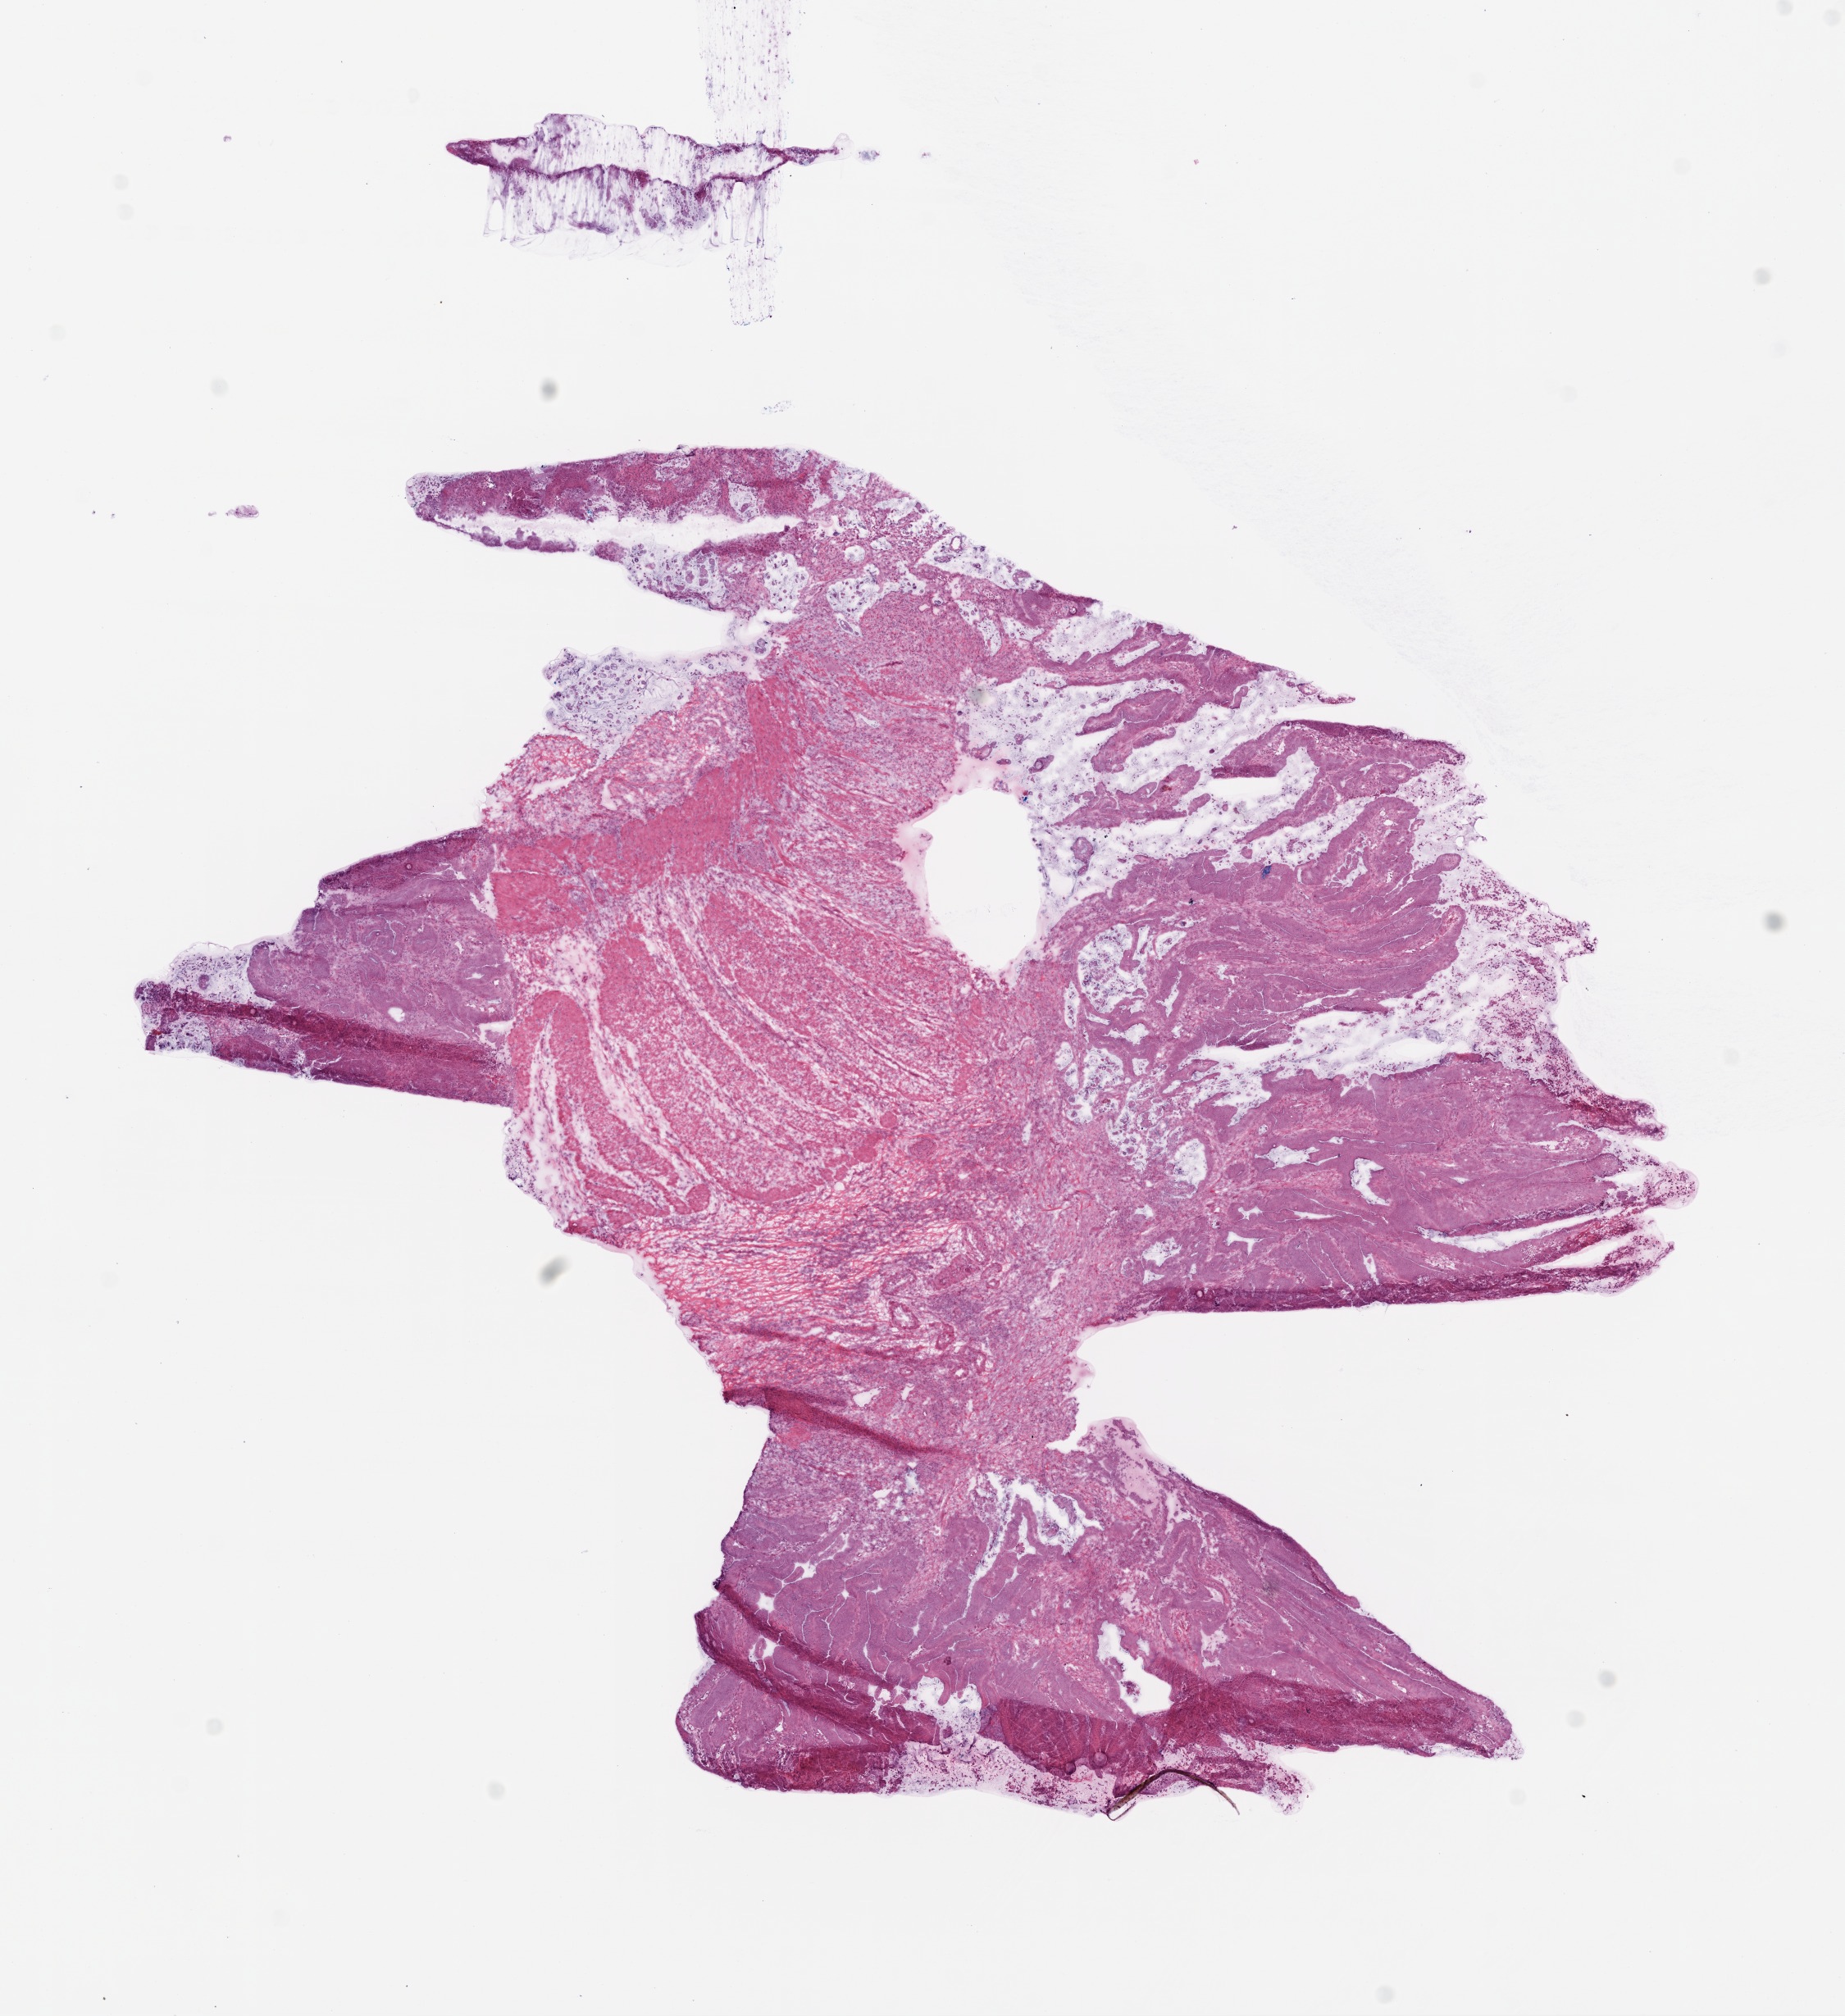
Hematoxylin and eosin (H&E) stained whole-slide image, shown as a low-resolution overview of the whole scanned area (about 9.0 x 9.9 mm), frozen section from the top of the tissue portion, colon, primary tumour sample. Female, age 83 years at initial diagnosis. Slide review estimates, as recorded: tumour cells 70%, tumour nuclei 70%.
Diagnosis: Mucinous adenocarcinoma (transverse colon).